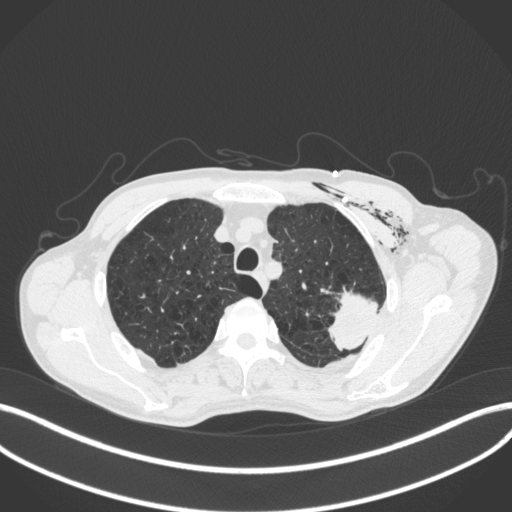
Chest CT, one axial slice; position 333 of 416 along the scan axis; 120 kVp; lung window (W 1500 / L -600 HU); 1 mm slice thickness; 512 × 512 image matrix, field of view 400 × 400 mm. Patient: male, 58 years. From the clinical record (not read from this slice): clinical TNM (as recorded): T3 N0 M0.
Structures marked on this image (rectangle marked by the reading radiologist):
- lung tumour (recorded histology: adenocarcinoma): bounding box [x1, y1, x2, y2] px = [324, 286, 380, 350]